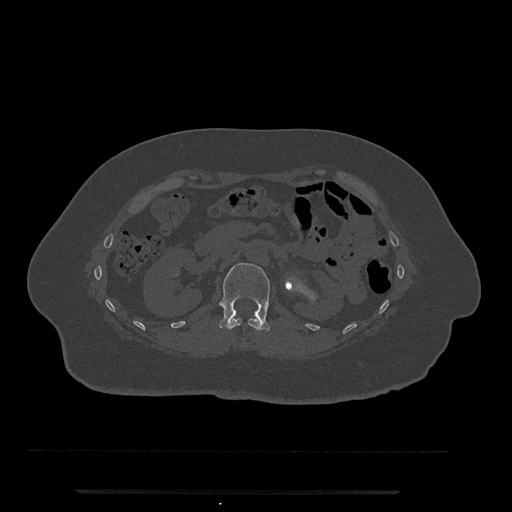
CT including the spine, one axial slice; position 122 of 797 along the scan axis; reconstruction kernel Br40s/3; 120 kVp; bone window (W 1800 / L 400 HU); 0.5 mm slice thickness; 512 × 512 image matrix. Female patient, age 51 years. Case-level facts recorded for this patient, not image findings: primary cancer: neuro.
Structures marked on this image (semi-automatically segmented with operator editing):
- L1 vertebra: bounding box <219,263,270,331> (left, top, right, bottom; pixels)
- T12 vertebra: <227,318,262,331>